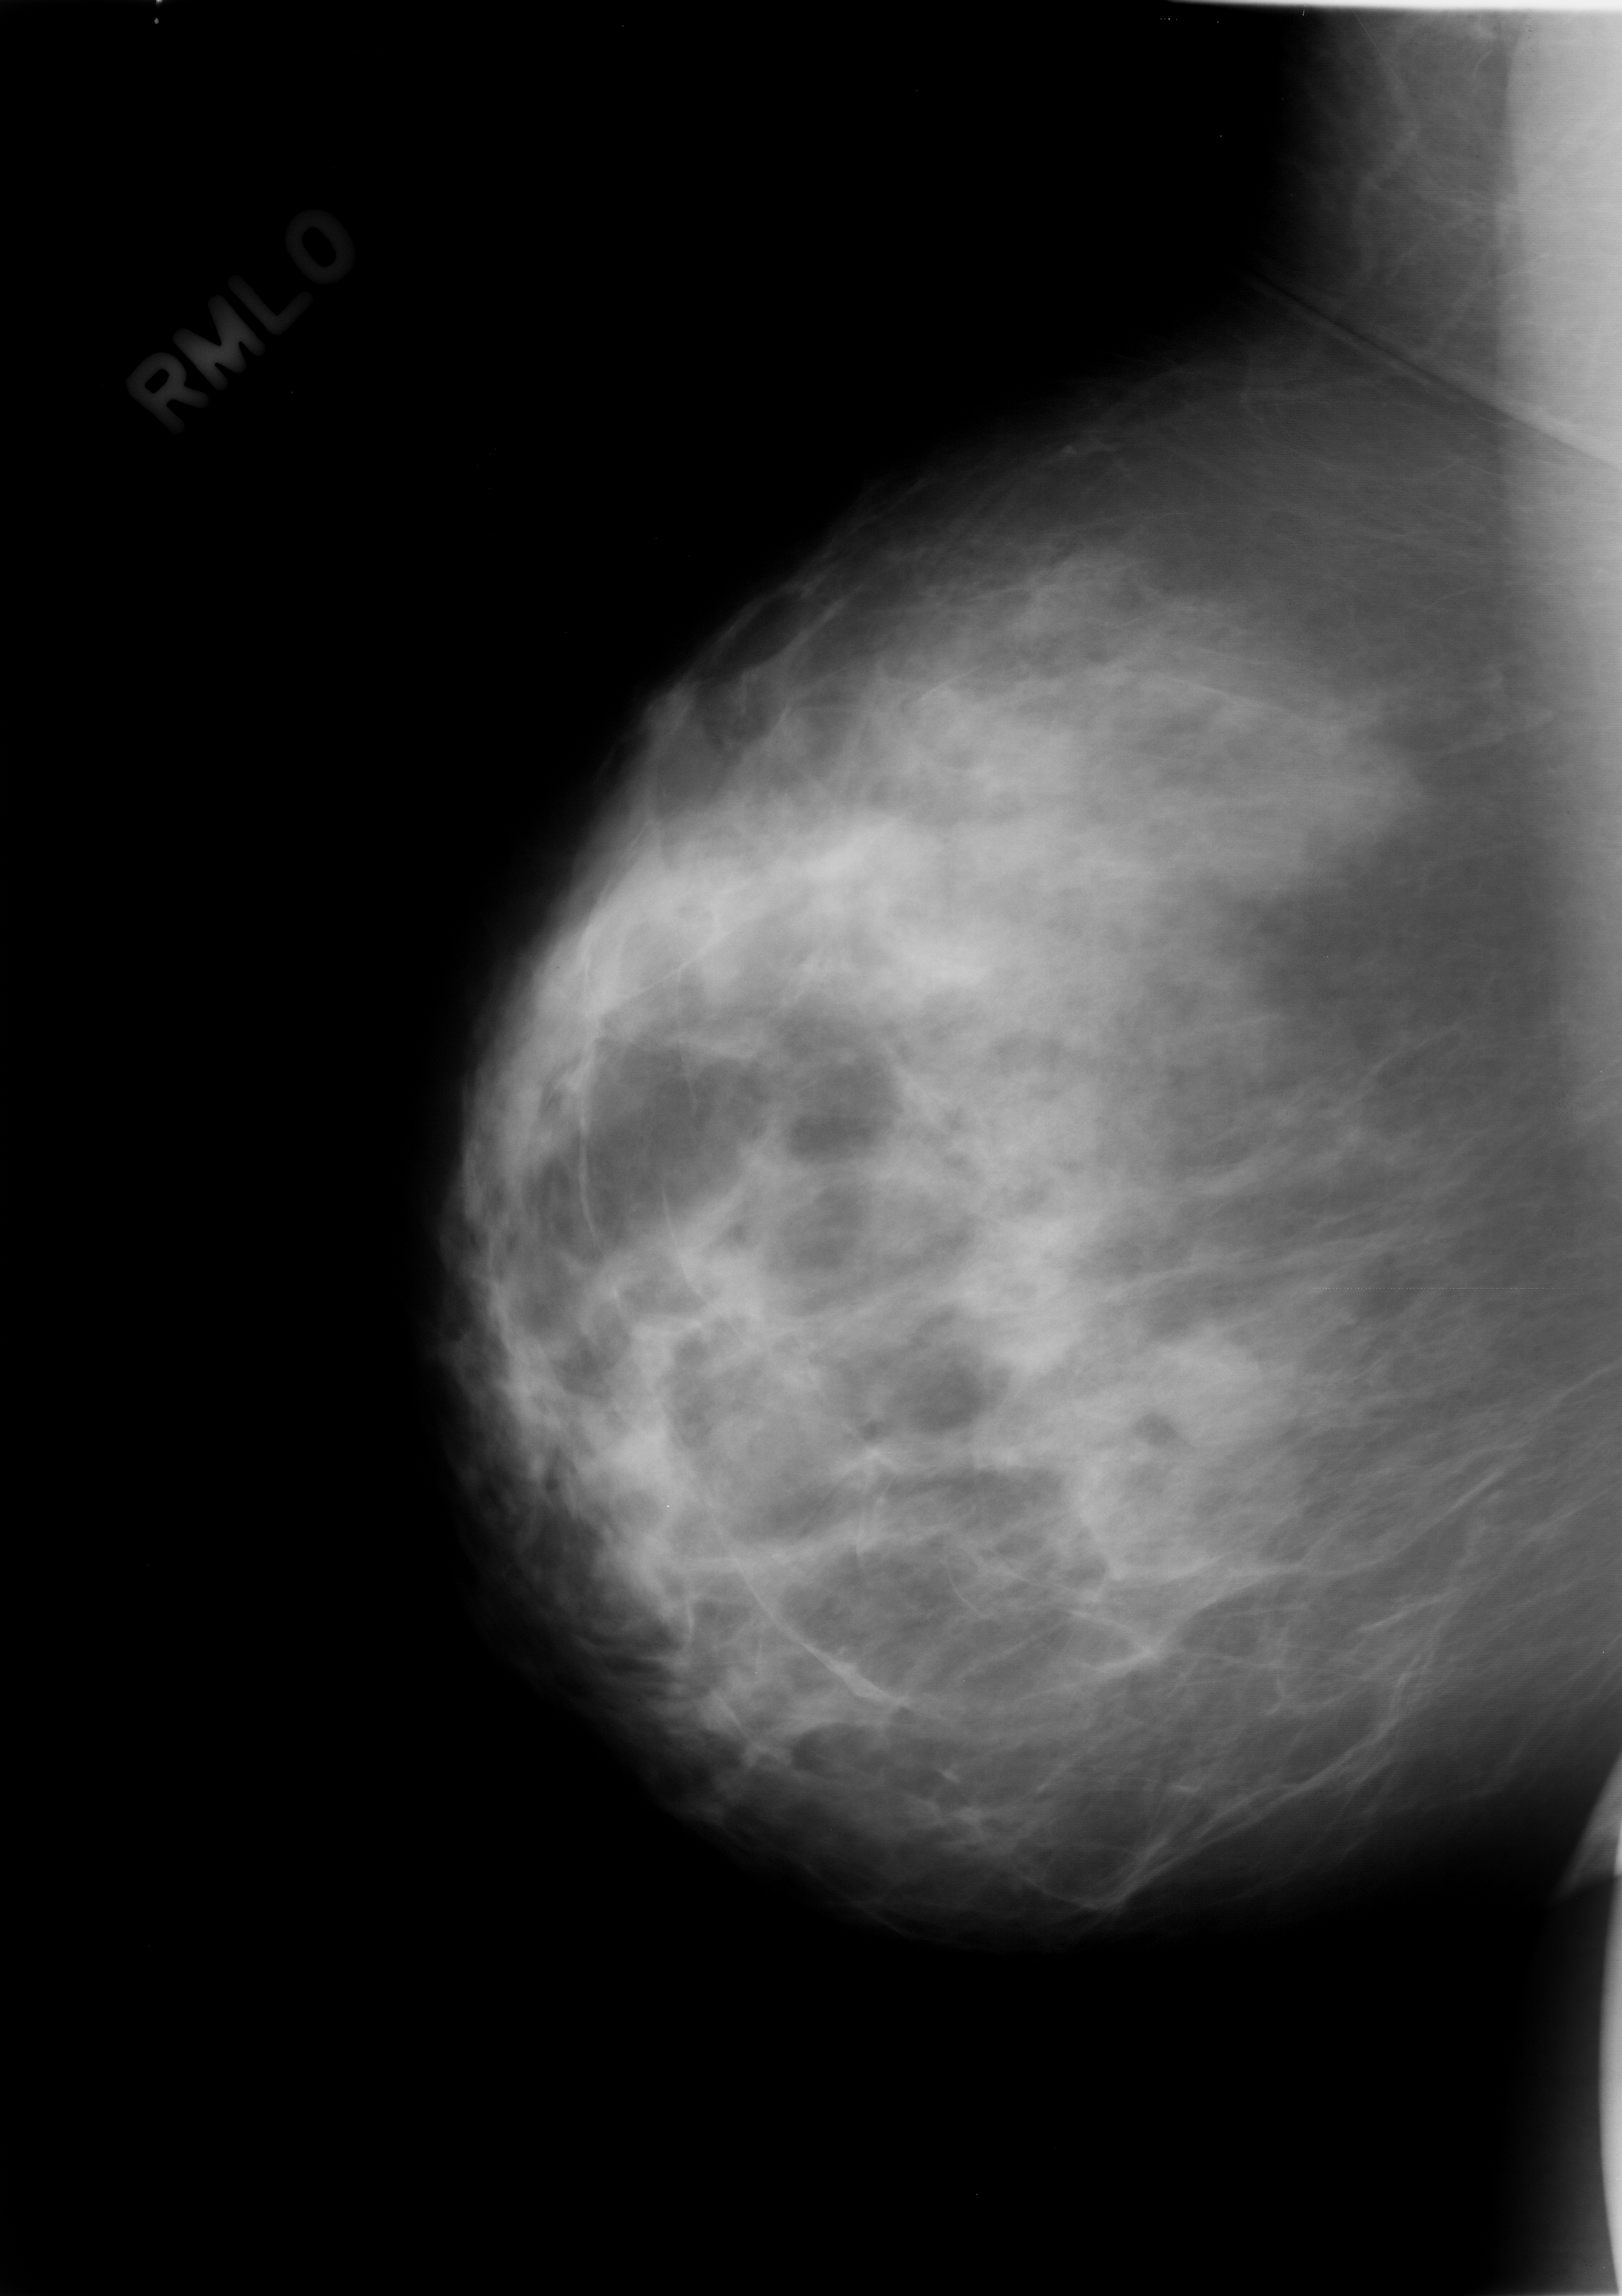
Mammogram (digitized film); right breast; MLO view; BI-RADS breast density category 2 (scale 1–4); 1622 × 2296 image matrix.
Expert-marked regions of interest on this image (one box per marked abnormality):
- mass, shape lobulated, margins circumscribed; BI-RADS assessment category 3; subtlety rating 4 on a 1 (subtle) to 5 (obvious) scale; pathology (as recorded): benign: bounding box (x1, y1, x2, y2) in pixels: (1143, 1320, 1273, 1452)